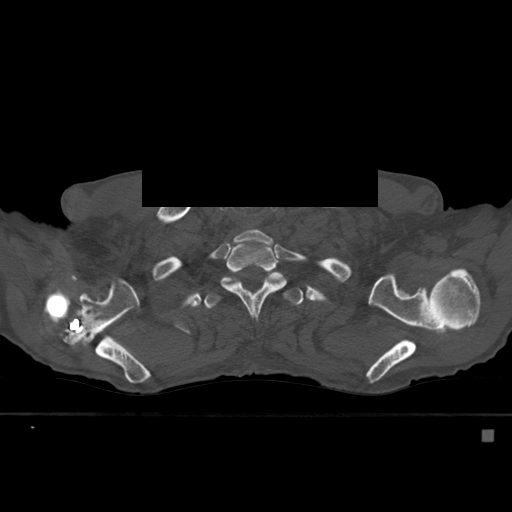
CT including the spine, one axial slice; position 444 of 527 along the scan axis; bone window (W 1800 / L 400 HU); 512 × 512 image matrix, field of view 373 × 373 mm. Male patient, age 78 years. From the clinical record (not read from this slice): primary cancer: prostate.
Structures marked on this image (semi-automatic segmentation, software-assisted and operator-edited):
- T1 vertebra: bounding box <240,227,273,244> (left, top, right, bottom; pixels)
- T2 vertebra: <221,234,286,317>
- T3 vertebra: <204,276,303,310>